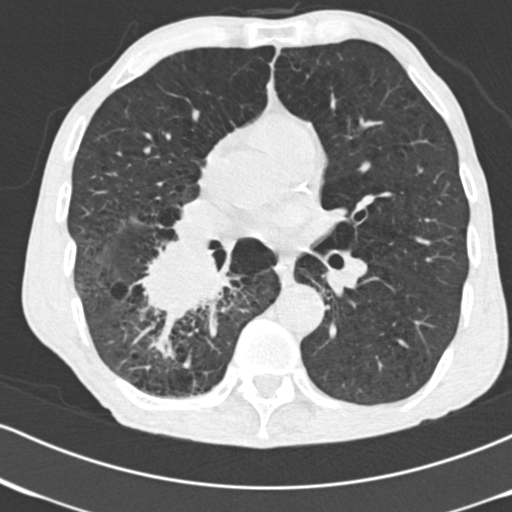
Low-dose screening chest CT, one axial slice. Slice 85 of 182 in the series (ordered by position). Reconstruction kernel B30f. 120 kVp. Lung window (W 1500 / L -600 HU). 2 mm slice thickness. 512 × 512 image matrix, field of view 316 × 316 mm.
Outlined on this slice (expert manual segmentation):
- lesion 1 (tumor, lower lobe of right lung): bounding box (x1, y1, x2, y2) in pixels: (141, 242, 229, 319)